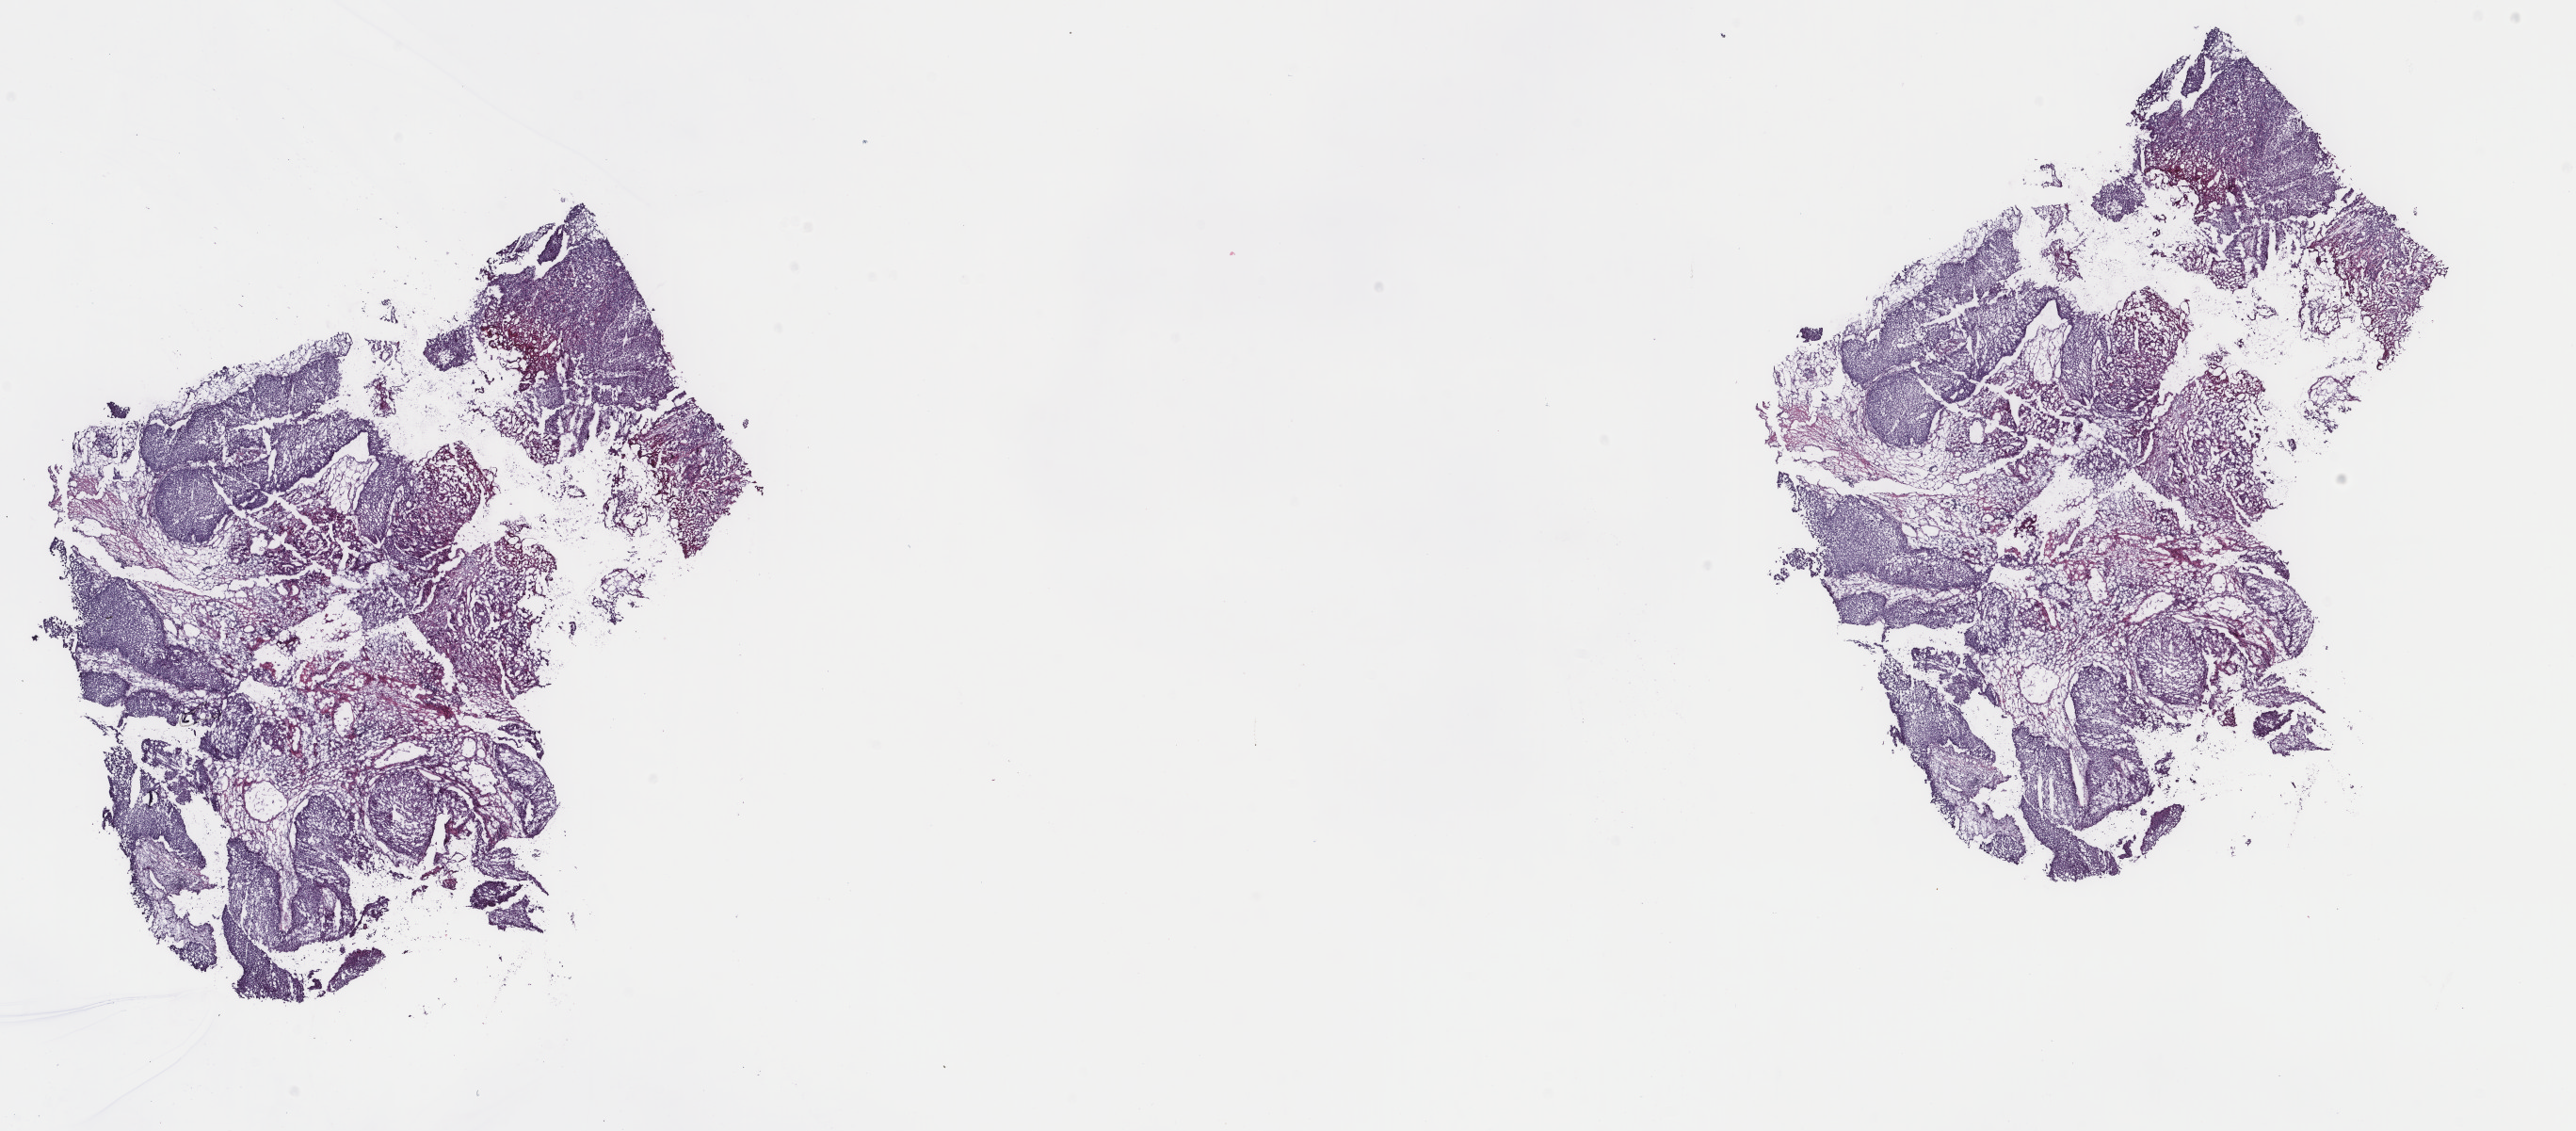
Digitized Hematoxylin and eosin (H&E) stained tissue section (whole slide), a low-resolution overview of the entire scanned area, about 21.7 x 9.5 mm (acquisition: 40x scan), frozen section from the top of the tissue portion, primary tumour sample from the bladder. Male, age 72 years at initial diagnosis. Histologic grade: high grade. Slide review estimates, as recorded: tumour cells 90%, tumour nuclei 80%, normal cells 0%, stromal cells 0%, necrosis 10%. Inflammatory infiltration, as recorded: lymphocyte infiltration 3%, monocyte infiltration 0%, neutrophil infiltration 0%.
• histologic diagnosis: Papillary transitional cell carcinoma (lateral wall of bladder)